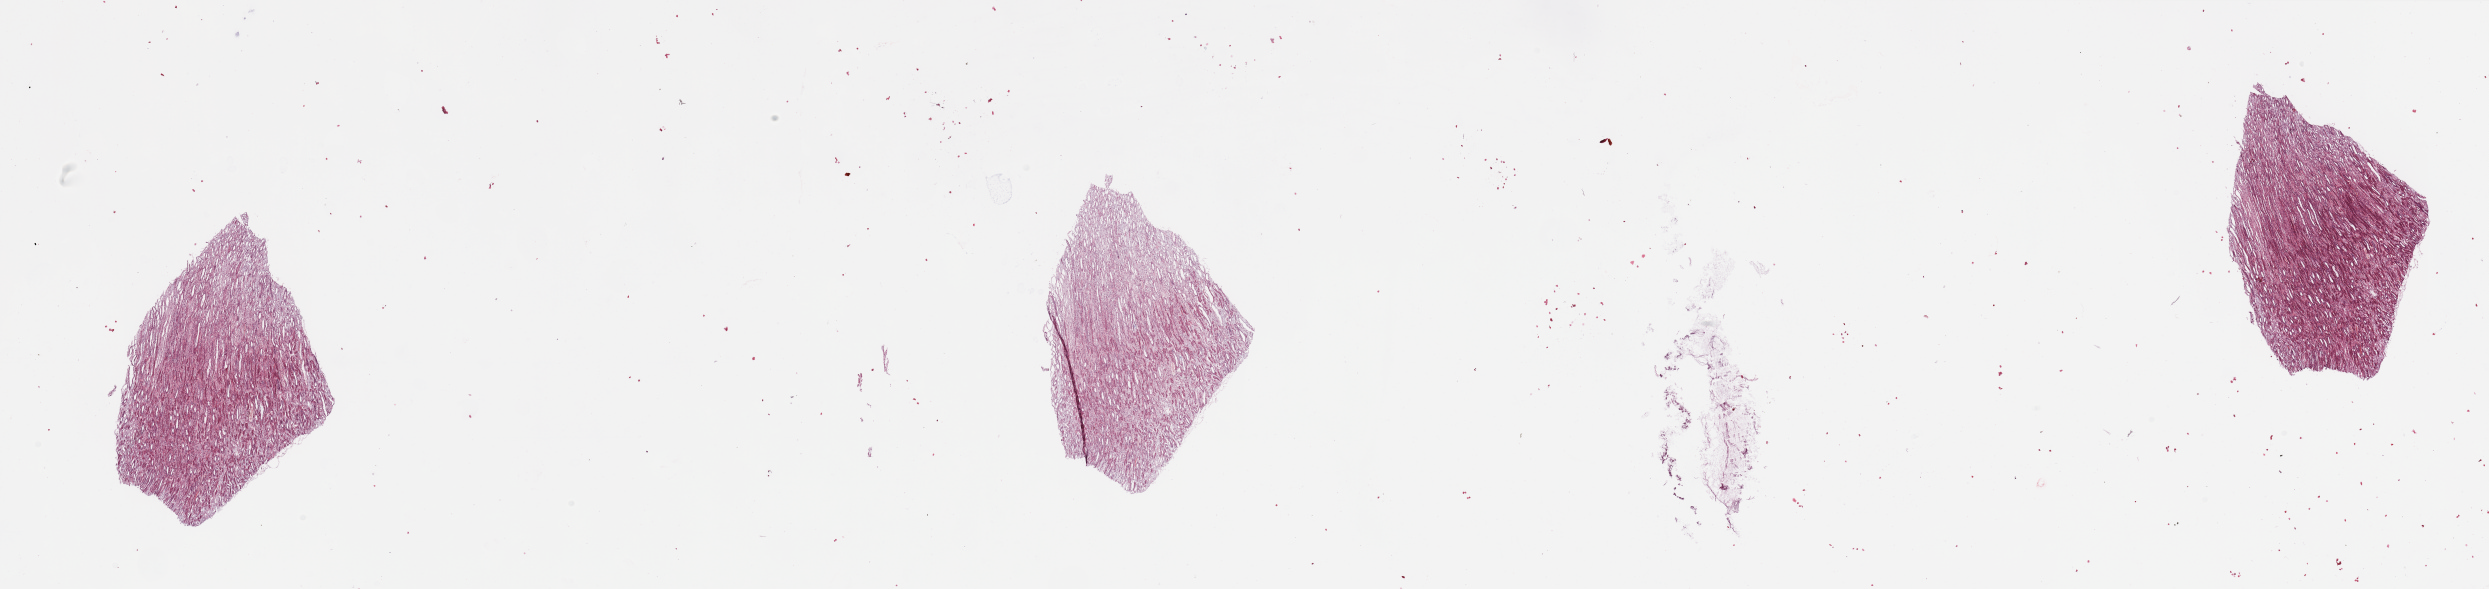
H&E whole-slide image — low-resolution overview of the scanned area, about 39.4 x 9.3 mm (from a 20x scan). Normal (non-tumour) tissue sample, sampled site: kidney. 51-year-old male patient.
This section: normal (non-tumour) tissue from the same patient. Patient diagnosis: Renal cell carcinoma, NOS.